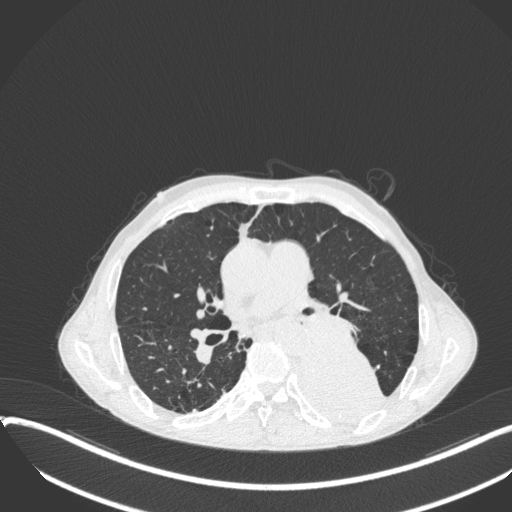
Chest CT, one axial slice. Slice 204 of 400 in the series (ordered by position). Reconstruction kernel B31f. 120 kVp. Lung window (W 1500 / L -600 HU). 512 × 512 image matrix, field of view 400 × 400 mm. Patient: male, 57 years. From the clinical record (not read from this slice): clinical TNM (as recorded): T4 N0 M0.
Structures marked on this image (bounding box drawn by a radiologist):
- lung tumour (recorded histology: squamous cell carcinoma): bounding box <294,336,390,427> (left, top, right, bottom; pixels)